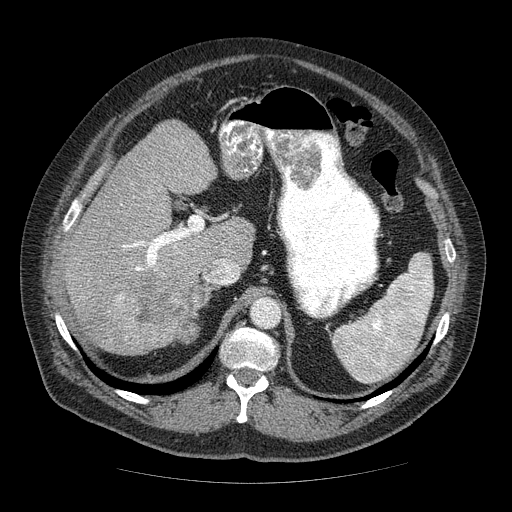
Contrast-enhanced abdominal CT (liver protocol), one axial slice; position 37 of 85 along the scan axis; soft-tissue window (W 400 / L 40 HU); 2.5 mm slice thickness; 512 × 512 image matrix, field of view 420 × 420 mm. Case-level facts recorded for this patient, not image findings: diagnosis: hepatocellular carcinoma (patient treated with transarterial chemoembolisation; whether this scan precedes or follows treatment is not stated here); TNM stage (as recorded): Stage-IIIA.
Structures marked on this image (semi-automatically segmented with operator editing):
- liver parenchyma outside the tumour (the mass and vessels are separate outlines, so this box may not span the whole liver): bounding box (x1, y1, x2, y2) in pixels: (64, 120, 254, 348)
- mass: (86, 267, 189, 356)
- liver vessels: (123, 232, 188, 271)